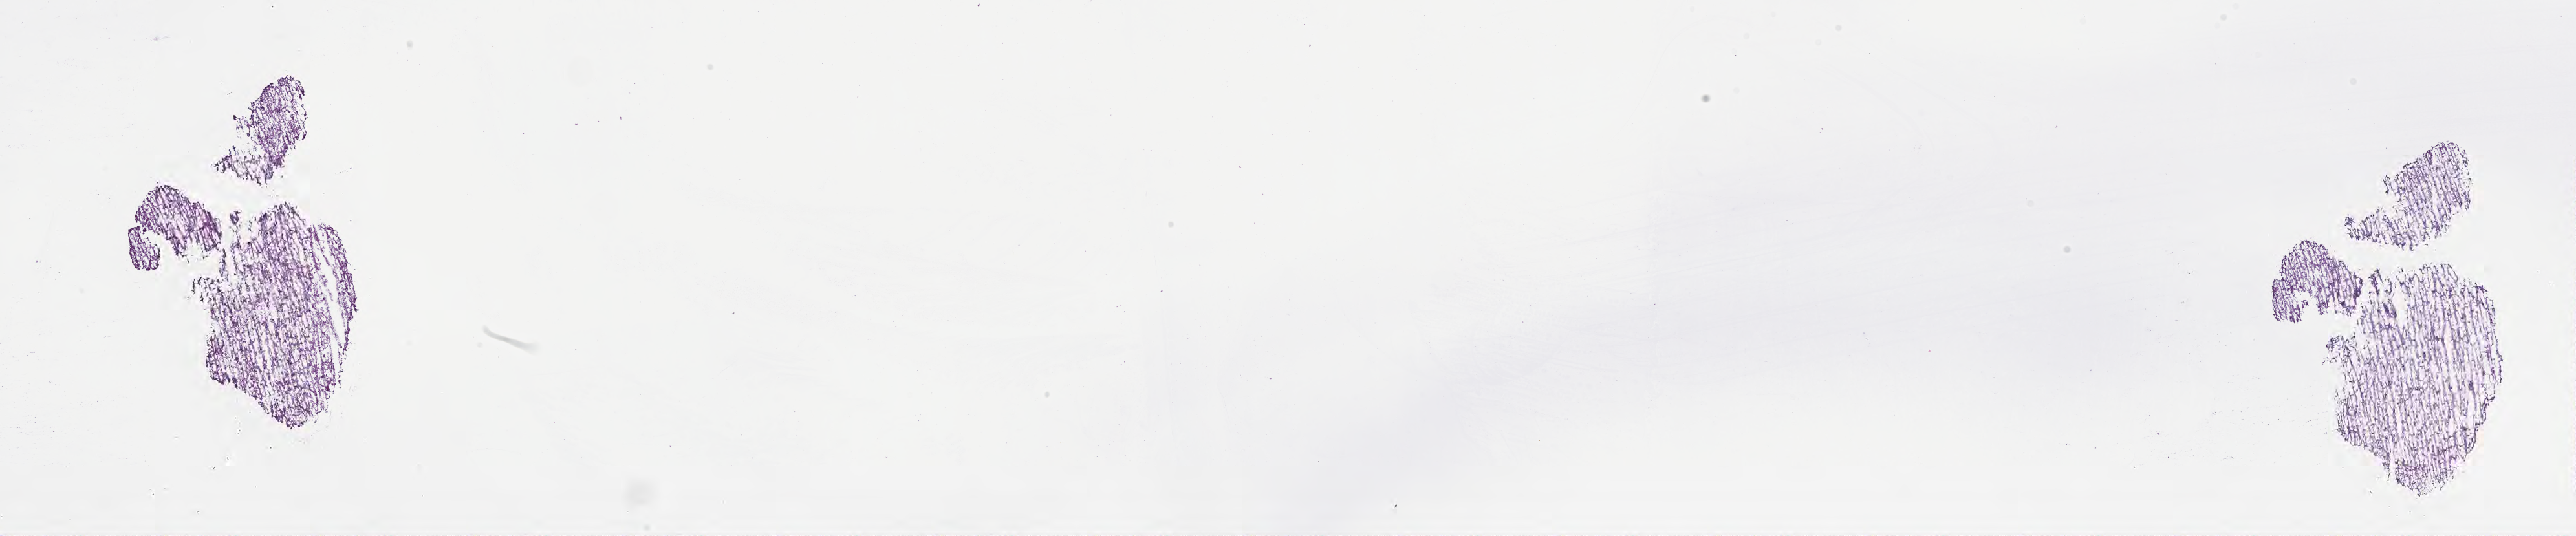
Whole-slide image, hematoxylin and eosin (H&E) stain of tumor tissue from the brain, shown as a low-resolution overview of the whole scanned area (about 32.2 x 6.7 mm); frozen section (OCT-embedded). Patient: female, age 69 months (5 years 9 months).
- diagnosis: Astrocytoma, NOS